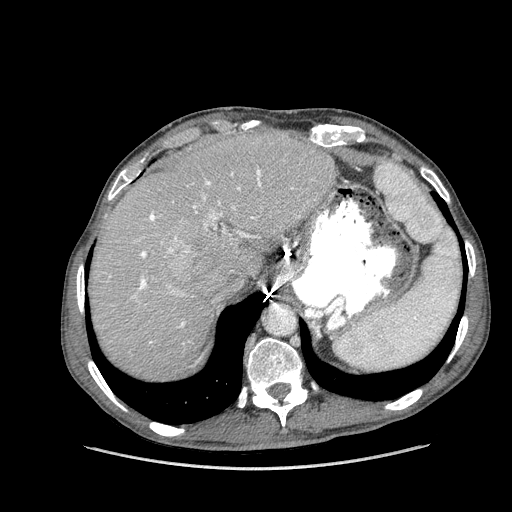
Contrast-enhanced abdominal CT (liver protocol), one axial slice; position 115 of 162 along the scan axis; soft-tissue window (W 400 / L 40 HU); 2.5 mm slice thickness; 512 × 512 image matrix, field of view 400 × 400 mm. Case-level facts recorded for this patient, not image findings: diagnosis: hepatocellular carcinoma (patient treated with transarterial chemoembolisation; whether this scan precedes or follows treatment is not stated here); TNM stage (as recorded): Stage-IIIA; Child-Pugh class: A; tumour size: 9.9 cm.
Structures marked on this image (semi-automatically segmented with operator editing):
- abdominal aorta: bounding box [x1, y1, x2, y2] px = [263, 303, 294, 335]
- liver parenchyma outside the tumour (the mass and vessels are separate outlines, so this box may not span the whole liver): [88, 132, 336, 378]
- mass: [167, 244, 216, 280]
- liver vessels: [132, 170, 300, 343]